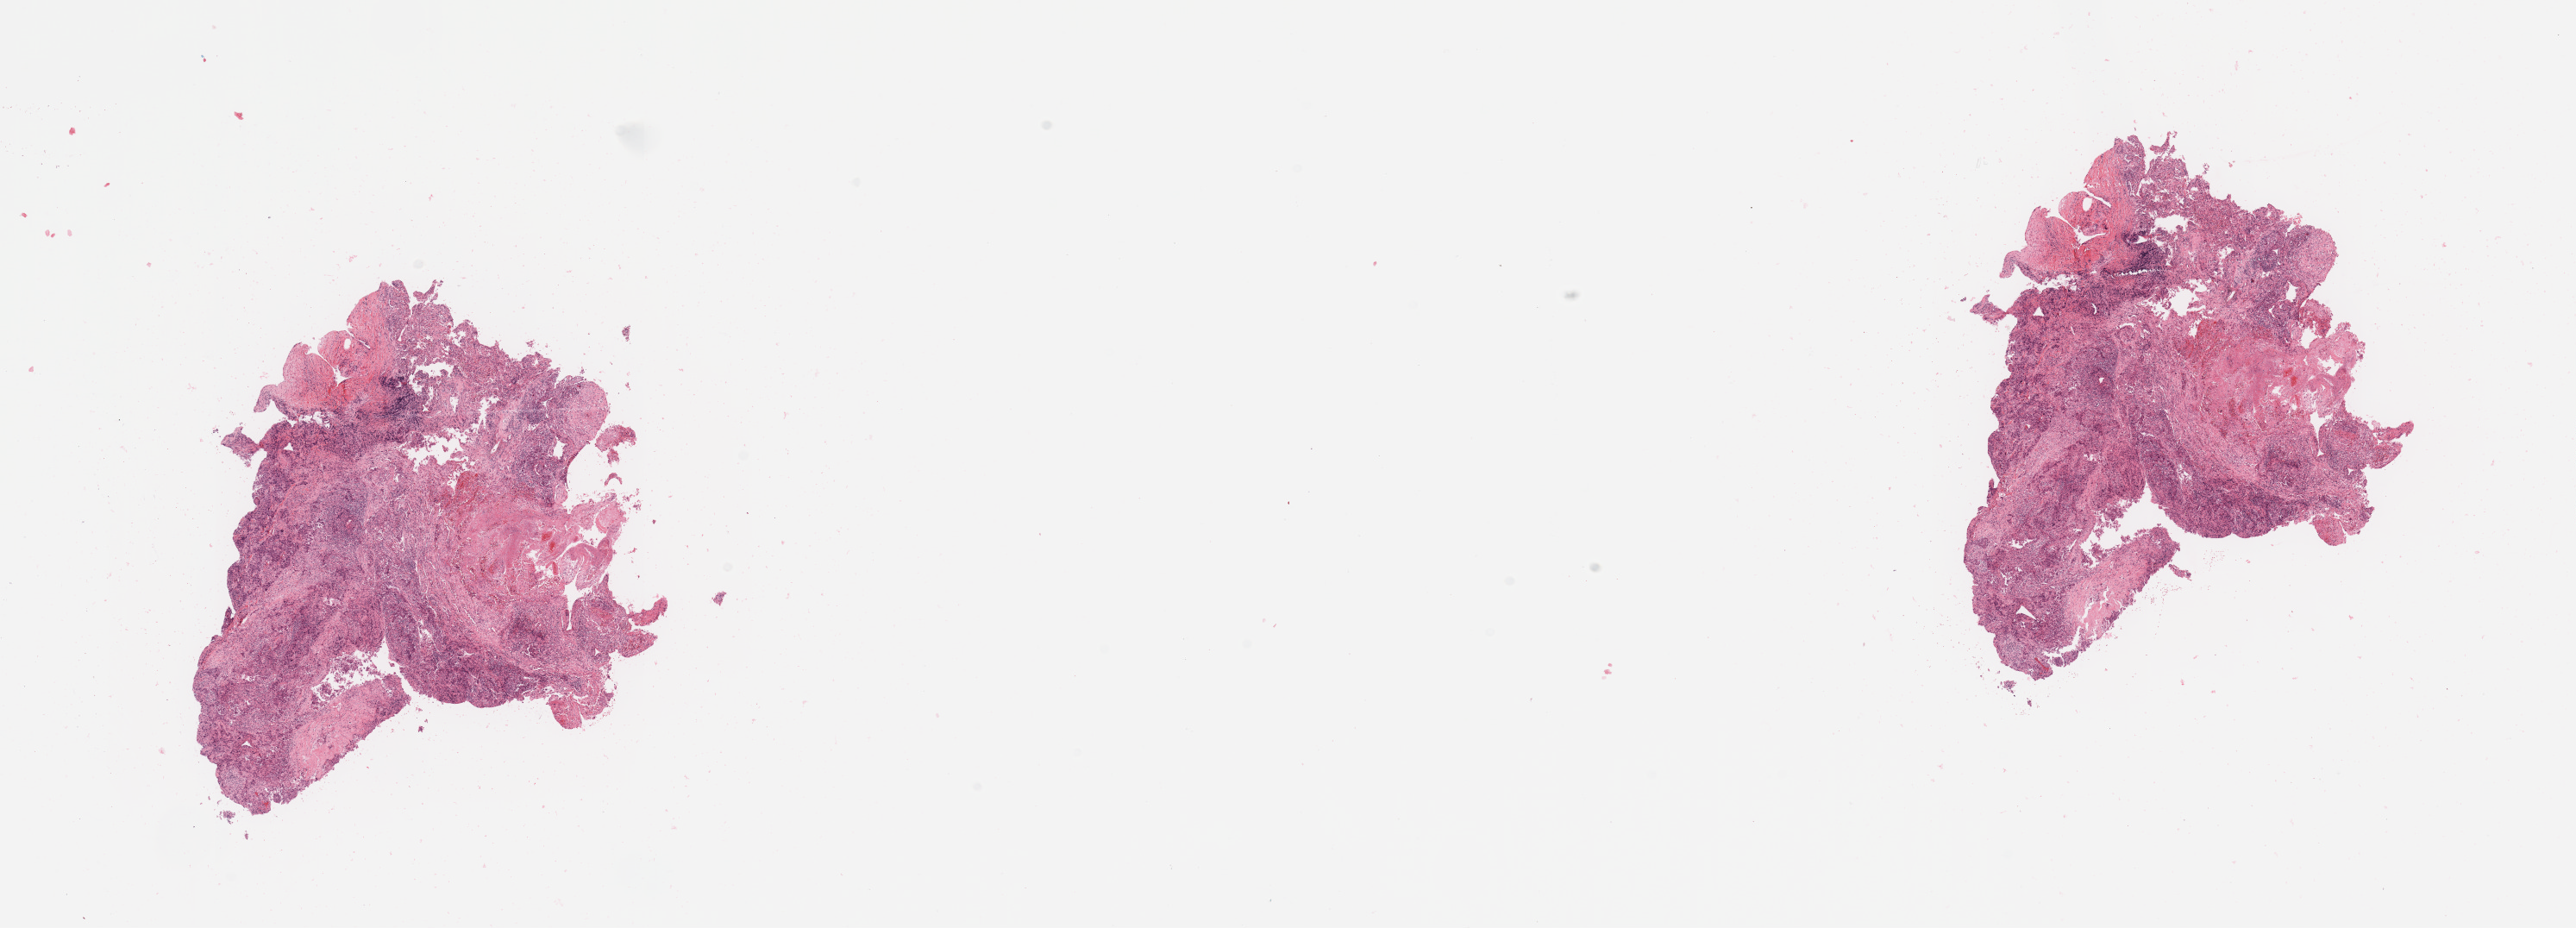
Whole-slide histology image, H&E-stained — whole scanned area (about 23.6 x 8.5 mm) shown as a low-resolution overview, tumour tissue sample, sampled site: lung. Female, 47 y/o. Histologic grade: G3 (poorly differentiated). Slide review estimates, as recorded: tumour nuclei 70%, necrosis 15%.
AJCC pathologic stage: IB. Primary tumour site (as recorded): right middle lobe. Histologic diagnosis: Adenocarcinoma, NOS.